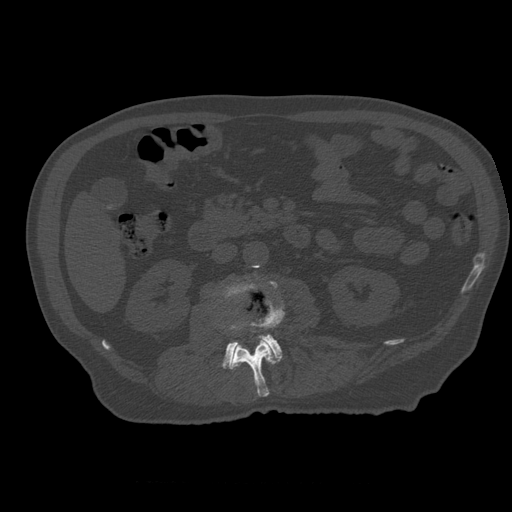
CT including the spine, one axial slice; position 203 of 399 along the scan axis; 120 kVp; bone window (W 1800 / L 400 HU); 512 × 512 image matrix, field of view 407 × 407 mm. Patient age 73 years. Case-level facts recorded for this patient, not image findings: primary cancer: prostate.
Structures marked on this image (semi-automatic segmentation, software-assisted and operator-edited):
- L2 vertebra: bounding box (x1, y1, x2, y2) in pixels: (230, 299, 285, 397)
- L3 vertebra: (223, 281, 285, 370)